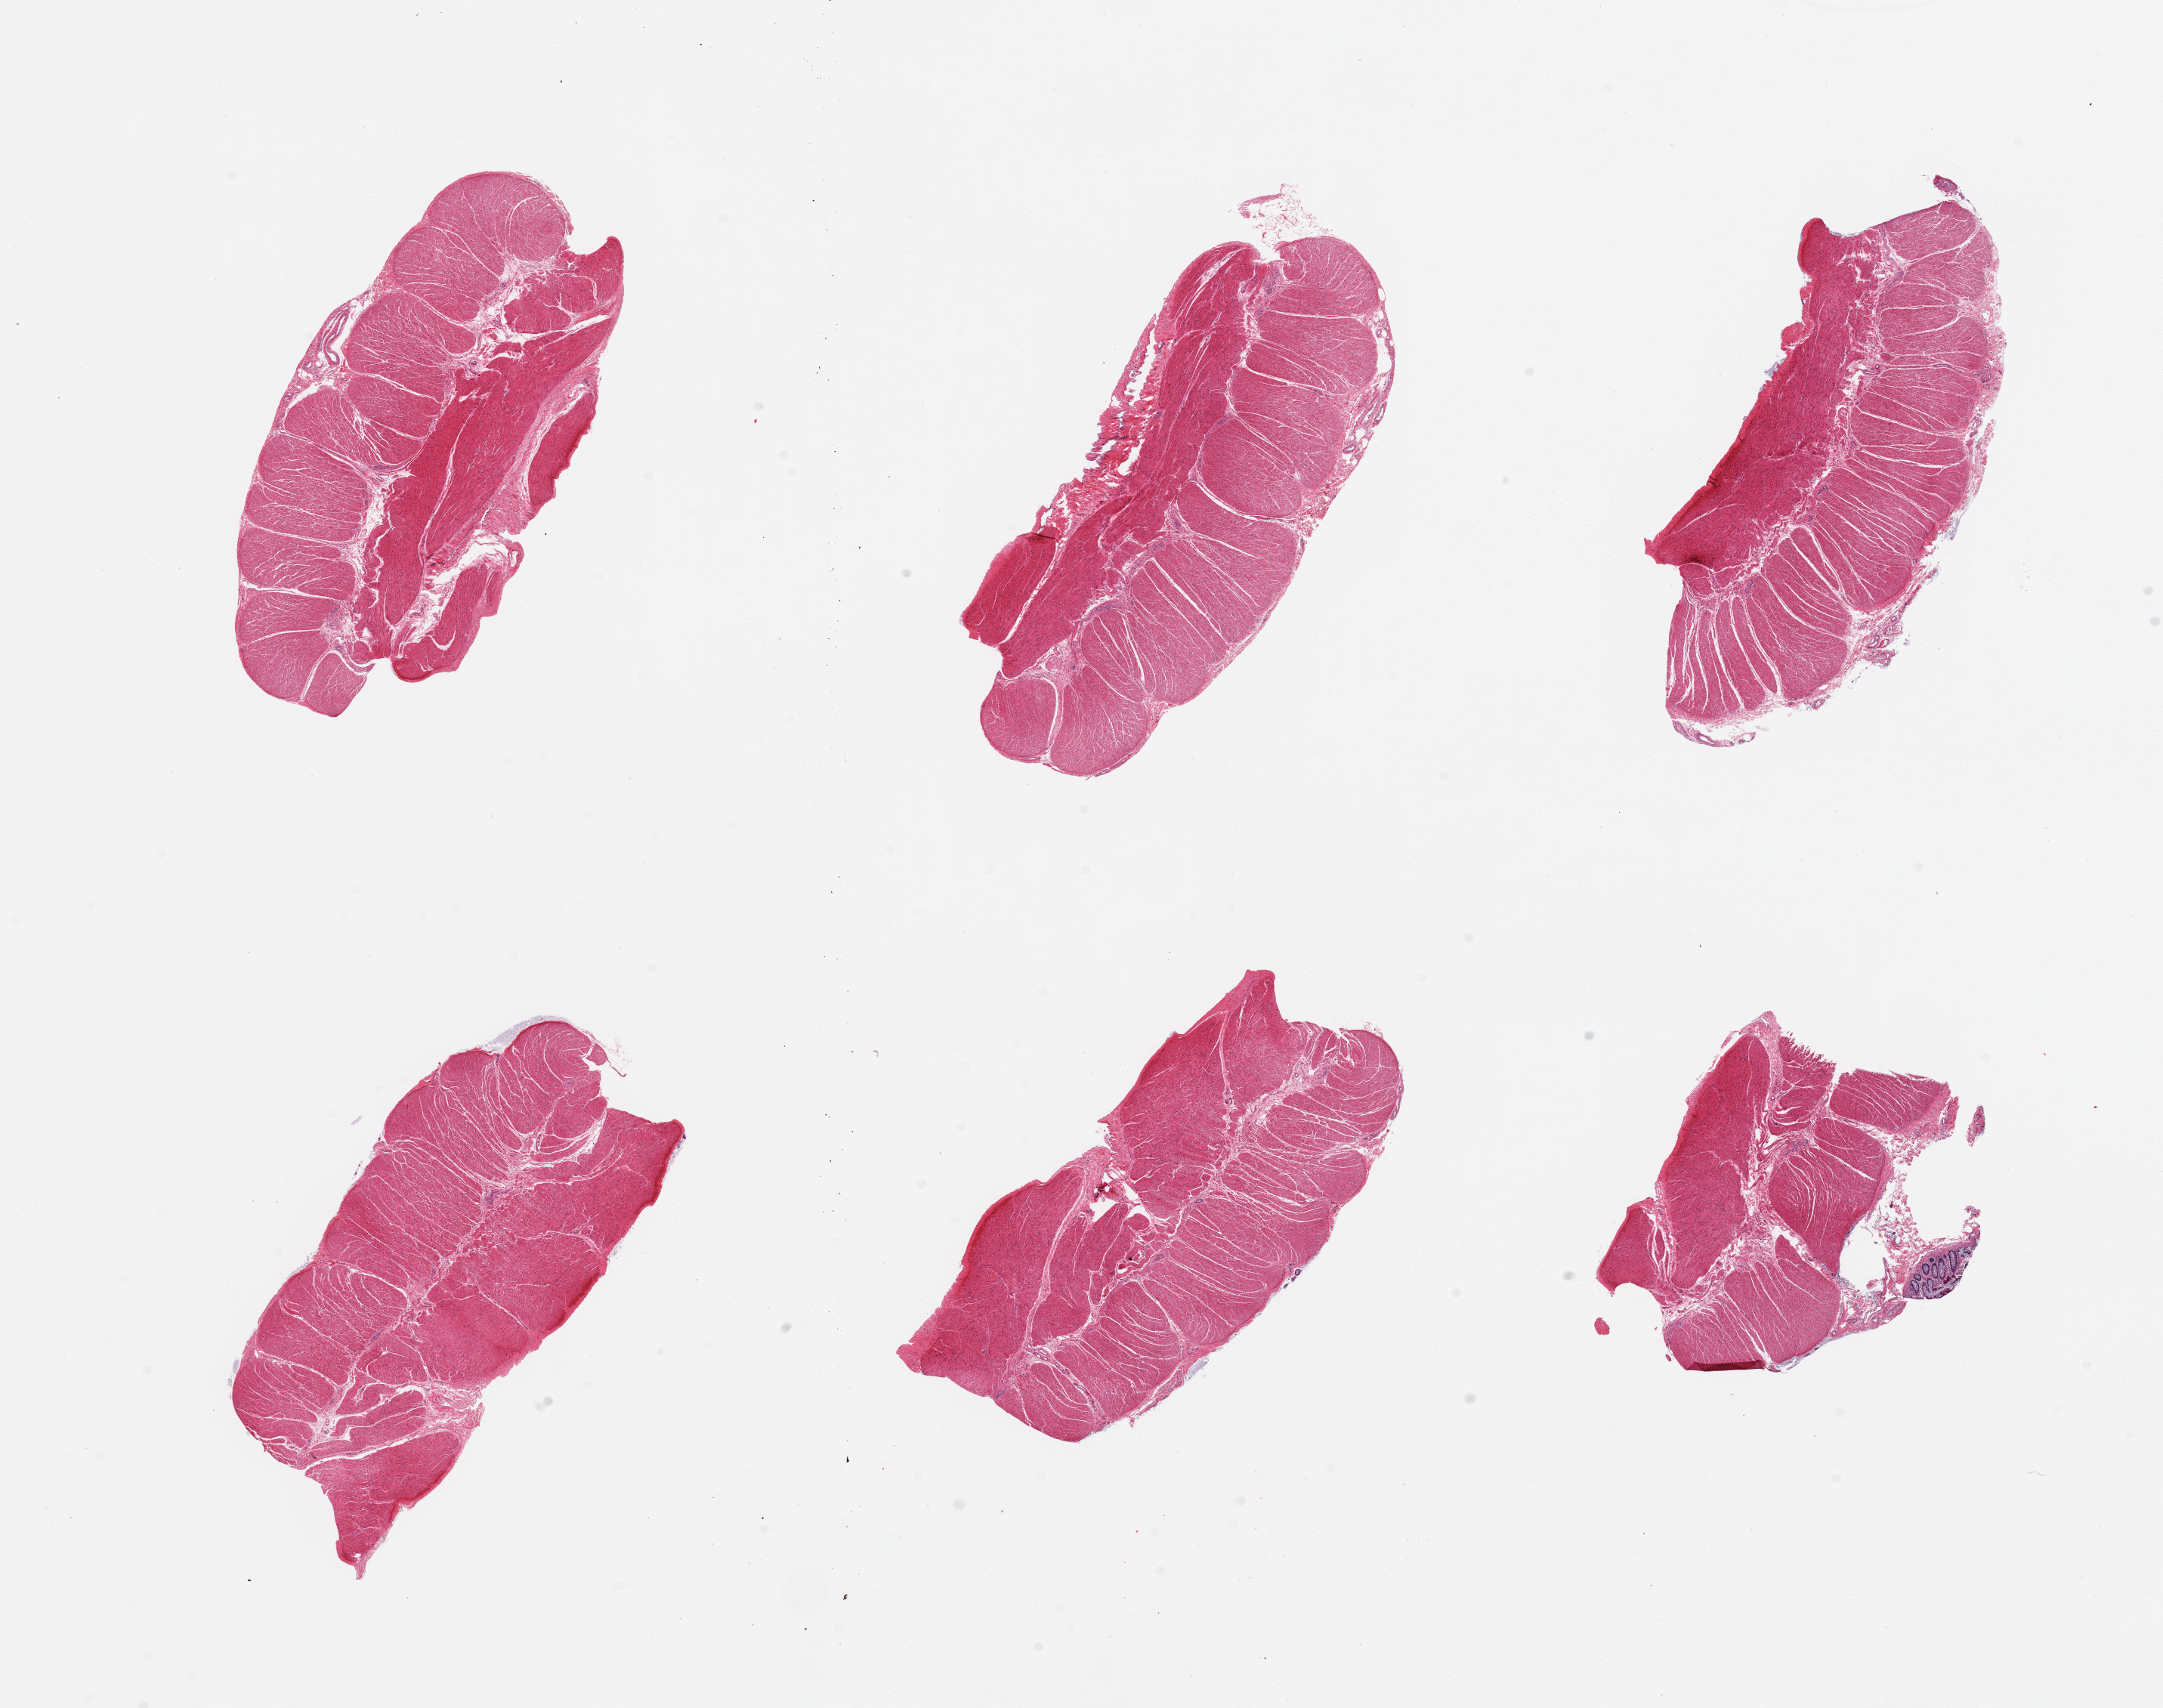
Whole-slide image, haematoxylin and eosin stain — a low-resolution overview of the entire scanned area, about 22.6 x 17.9 mm (slide scanned at 20x), PAXgene-fixed paraffin-embedded (PFPE) section, sampled site (target tissue): sigmoid colon, donor tissue sample. Donor sex: female.
• pathologist's review note for this sample: 6 pieces; target muscularis with small strip of residual mucosa on 1 piece